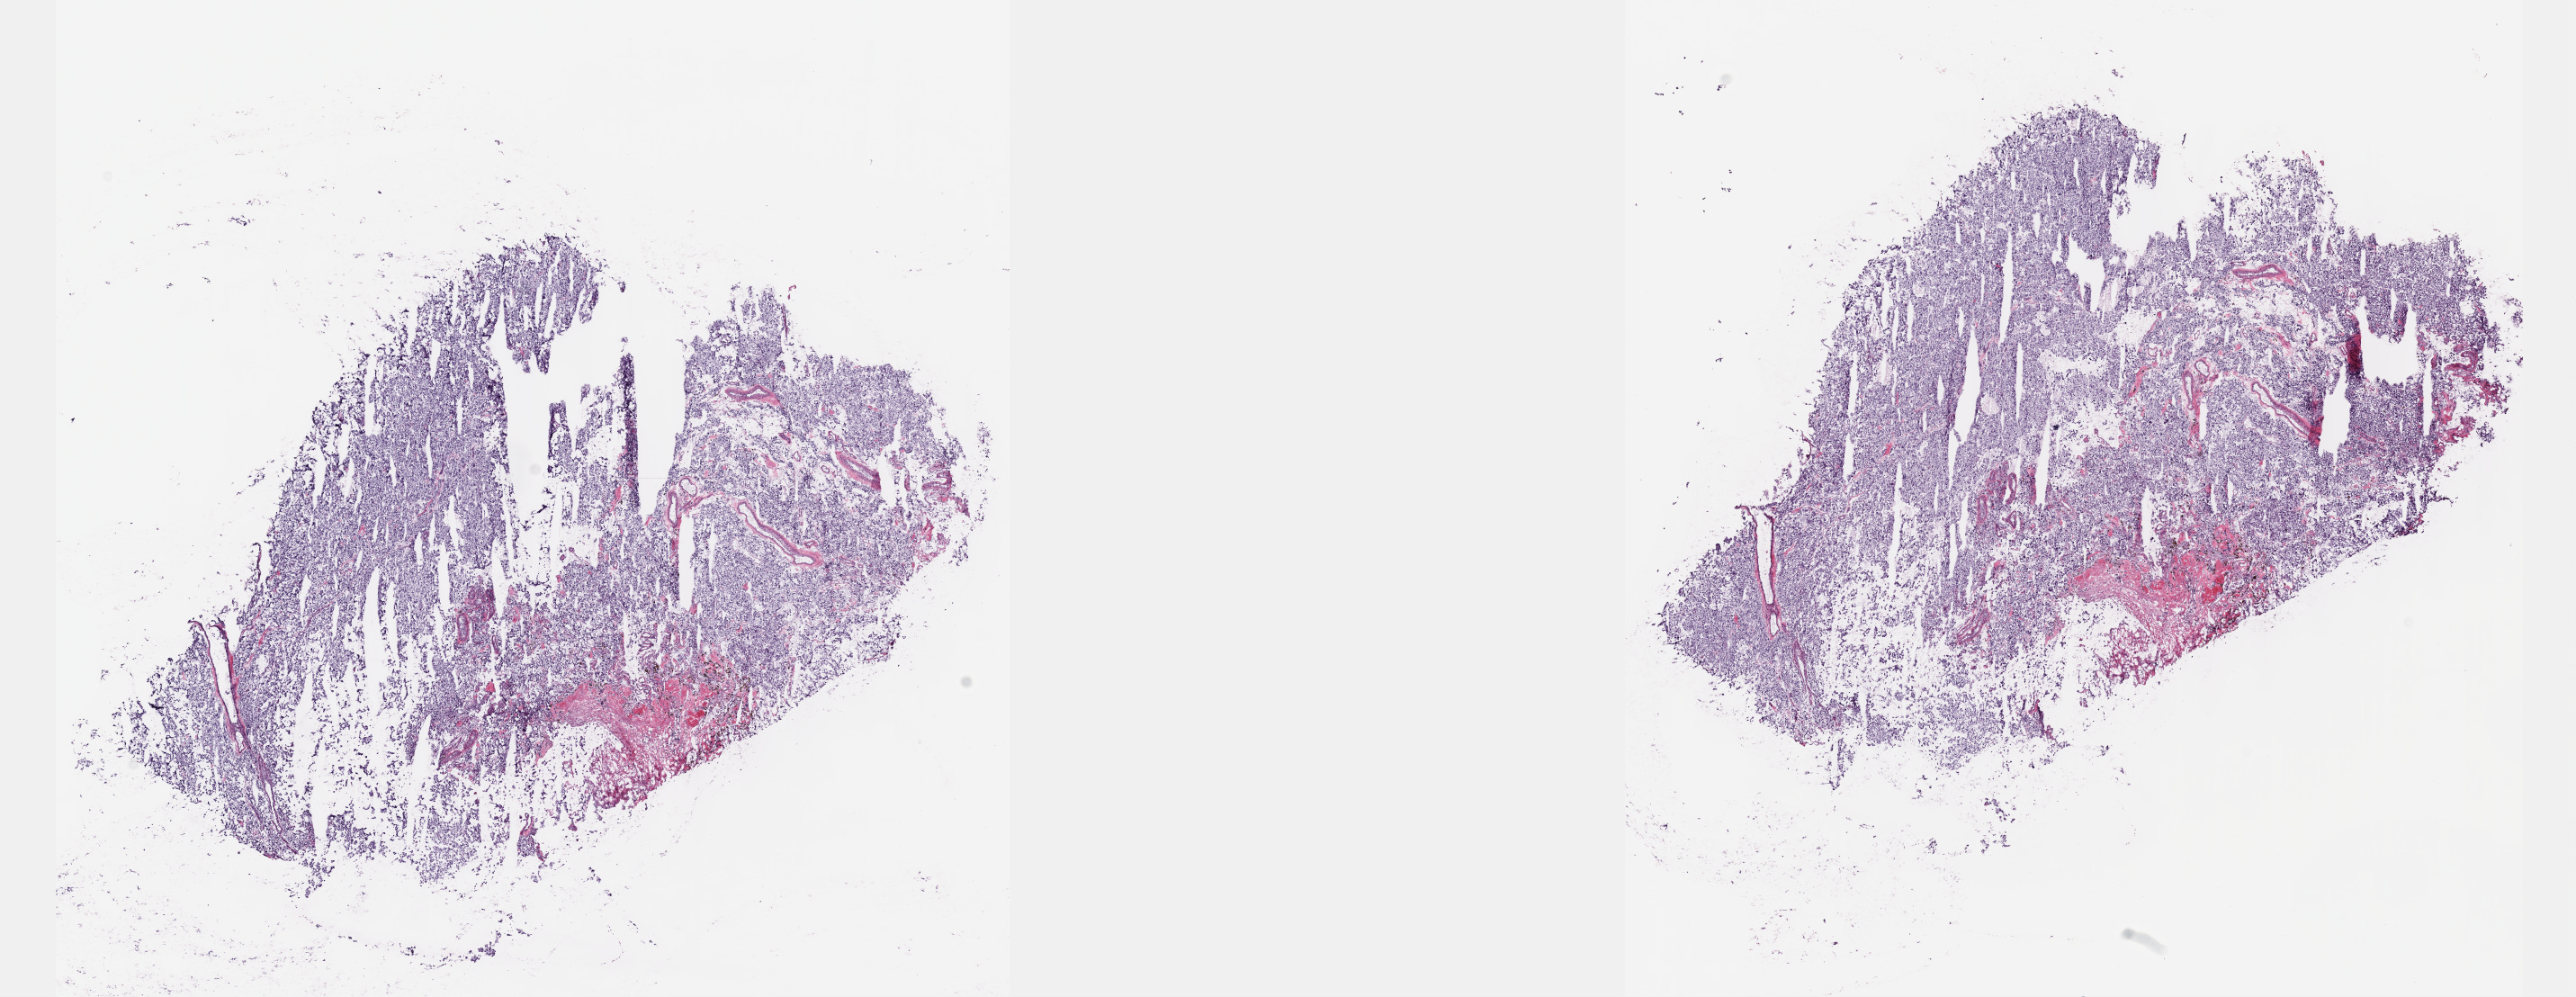
Whole-slide histology image, H&E — a low-resolution overview of the entire scanned area, about 23.1 x 9.0 mm. Frozen section from the top of the tissue portion. Sample: primary tumour, adrenal gland. Patient: female, age at initial diagnosis 57 years. Pathologist review of this section (percent, as recorded): tumour cells 80%, tumour nuclei 80%, normal cells 0%, stromal cells 10%, necrosis 10%. Inflammatory infiltration, as recorded: lymphocyte infiltration 40%, monocyte infiltration 20%, neutrophil infiltration 20%.
- histologic diagnosis: Pheochromocytoma, NOS